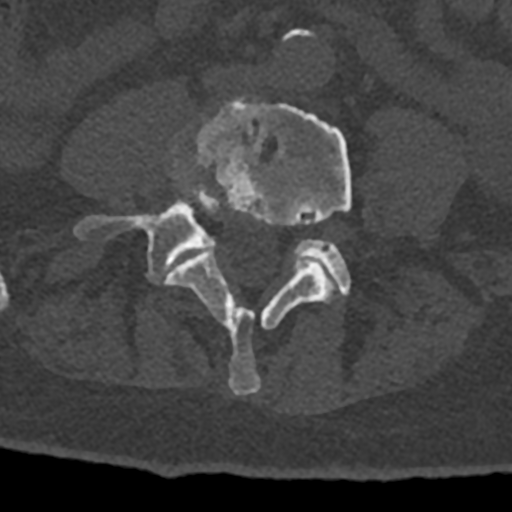
CT including the spine, one axial slice. Position 236 of 797 along the scan axis. 120 kVp. Bone window (W 1800 / L 400 HU). 0.5 mm slice thickness. 512 × 512 image matrix, field of view 160 × 160 mm. Patient: male, 74 years. Case-level facts recorded for this patient, not image findings: primary cancer: renal; vertebrae with lytic lesions (as recorded): T10, L1, L2, L3, L4, L5.
Structures marked on this image (semi-automatically segmented with operator editing):
- L4 vertebra: bounding box (x1, y1, x2, y2) in pixels: (165, 98, 351, 395)
- L5 vertebra: (74, 163, 350, 295)